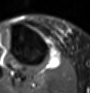
MRI of an extremity soft-tissue mass, one axial slice. Slice 41 of 60 in the series (ordered by position). STIR. MR volume resampled by the dataset authors to the PET/CT grid (not the native acquisition matrix). 3.27 mm slice thickness. 90 × 93 image matrix, field of view 88 × 91 mm. Female patient. Case-level facts recorded for this patient, not image findings: histological type: undifferentiated – high grade; grade: high; site of the primary tumour: right thigh.
Outlined on this slice (expert contour drawn on MRI and transferred to this co-registered scan by the dataset authors):
- gross tumour volume (mass): bounding box <47,49,61,70> (left, top, right, bottom; pixels)